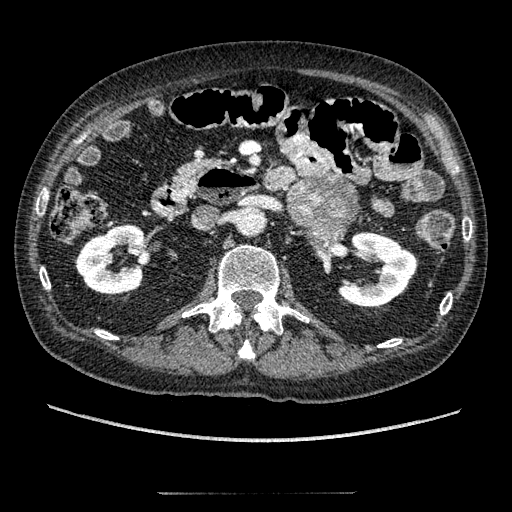
Contrast-enhanced abdominal CT, one axial slice. Position 92 of 274 along the scan axis. Reconstruction kernel STANDARD. 120 kVp. Intravenous contrast given. Soft-tissue window (W 400 / L 40 HU). 512 × 512 image matrix. Male patient, age 69 years. Case-level facts recorded for this patient, not image findings: diagnosis: adrenocortical carcinoma; tumour side: left adrenal; tumour size at pathology: 6.1 cm; Ki-67 index: 10 %; stage (as recorded): 3.
Structures marked on this image (semi-automatic segmentation, software-assisted and operator-edited):
- mass: bounding box <291,181,355,240> (left, top, right, bottom; pixels)